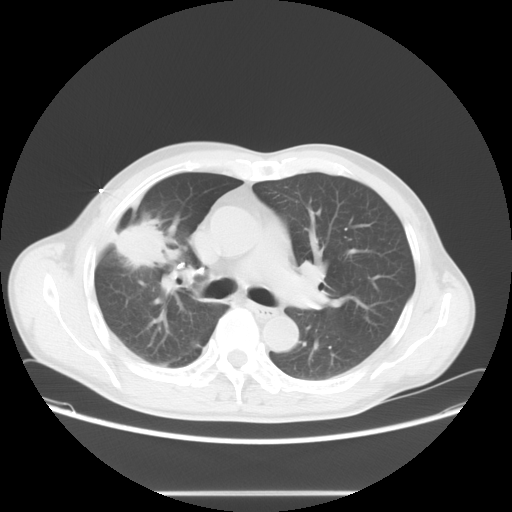
Chest CT, one axial slice. Slice 44 of 71 in the series (ordered by position). Lung window (W 1500 / L -600 HU). 512 × 512 image matrix, field of view 392 × 392 mm. Patient: male, 67 years. From the clinical record (not read from this slice): clinical TNM (as recorded): T2 N0 M0.
Annotated regions visible in this slice (rectangle marked by the reading radiologist):
- lung tumour (recorded histology: adenocarcinoma): bounding box [x1, y1, x2, y2] px = [117, 221, 172, 270]